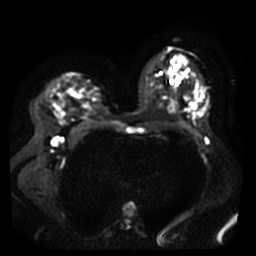
Breast MRI, one axial slice. Diffusion-weighted series; image 2 of 4 stored at this slice position (different b-values; order by instance number). 3 T. 5 mm slice thickness. 256 × 256 image matrix, field of view 360 × 360 mm. Female patient.
Annotated regions visible in this slice (manually delineated by an expert):
- tumour on diffusion-weighted imaging: bounding box (x1, y1, x2, y2) in pixels: (56, 110, 64, 118)